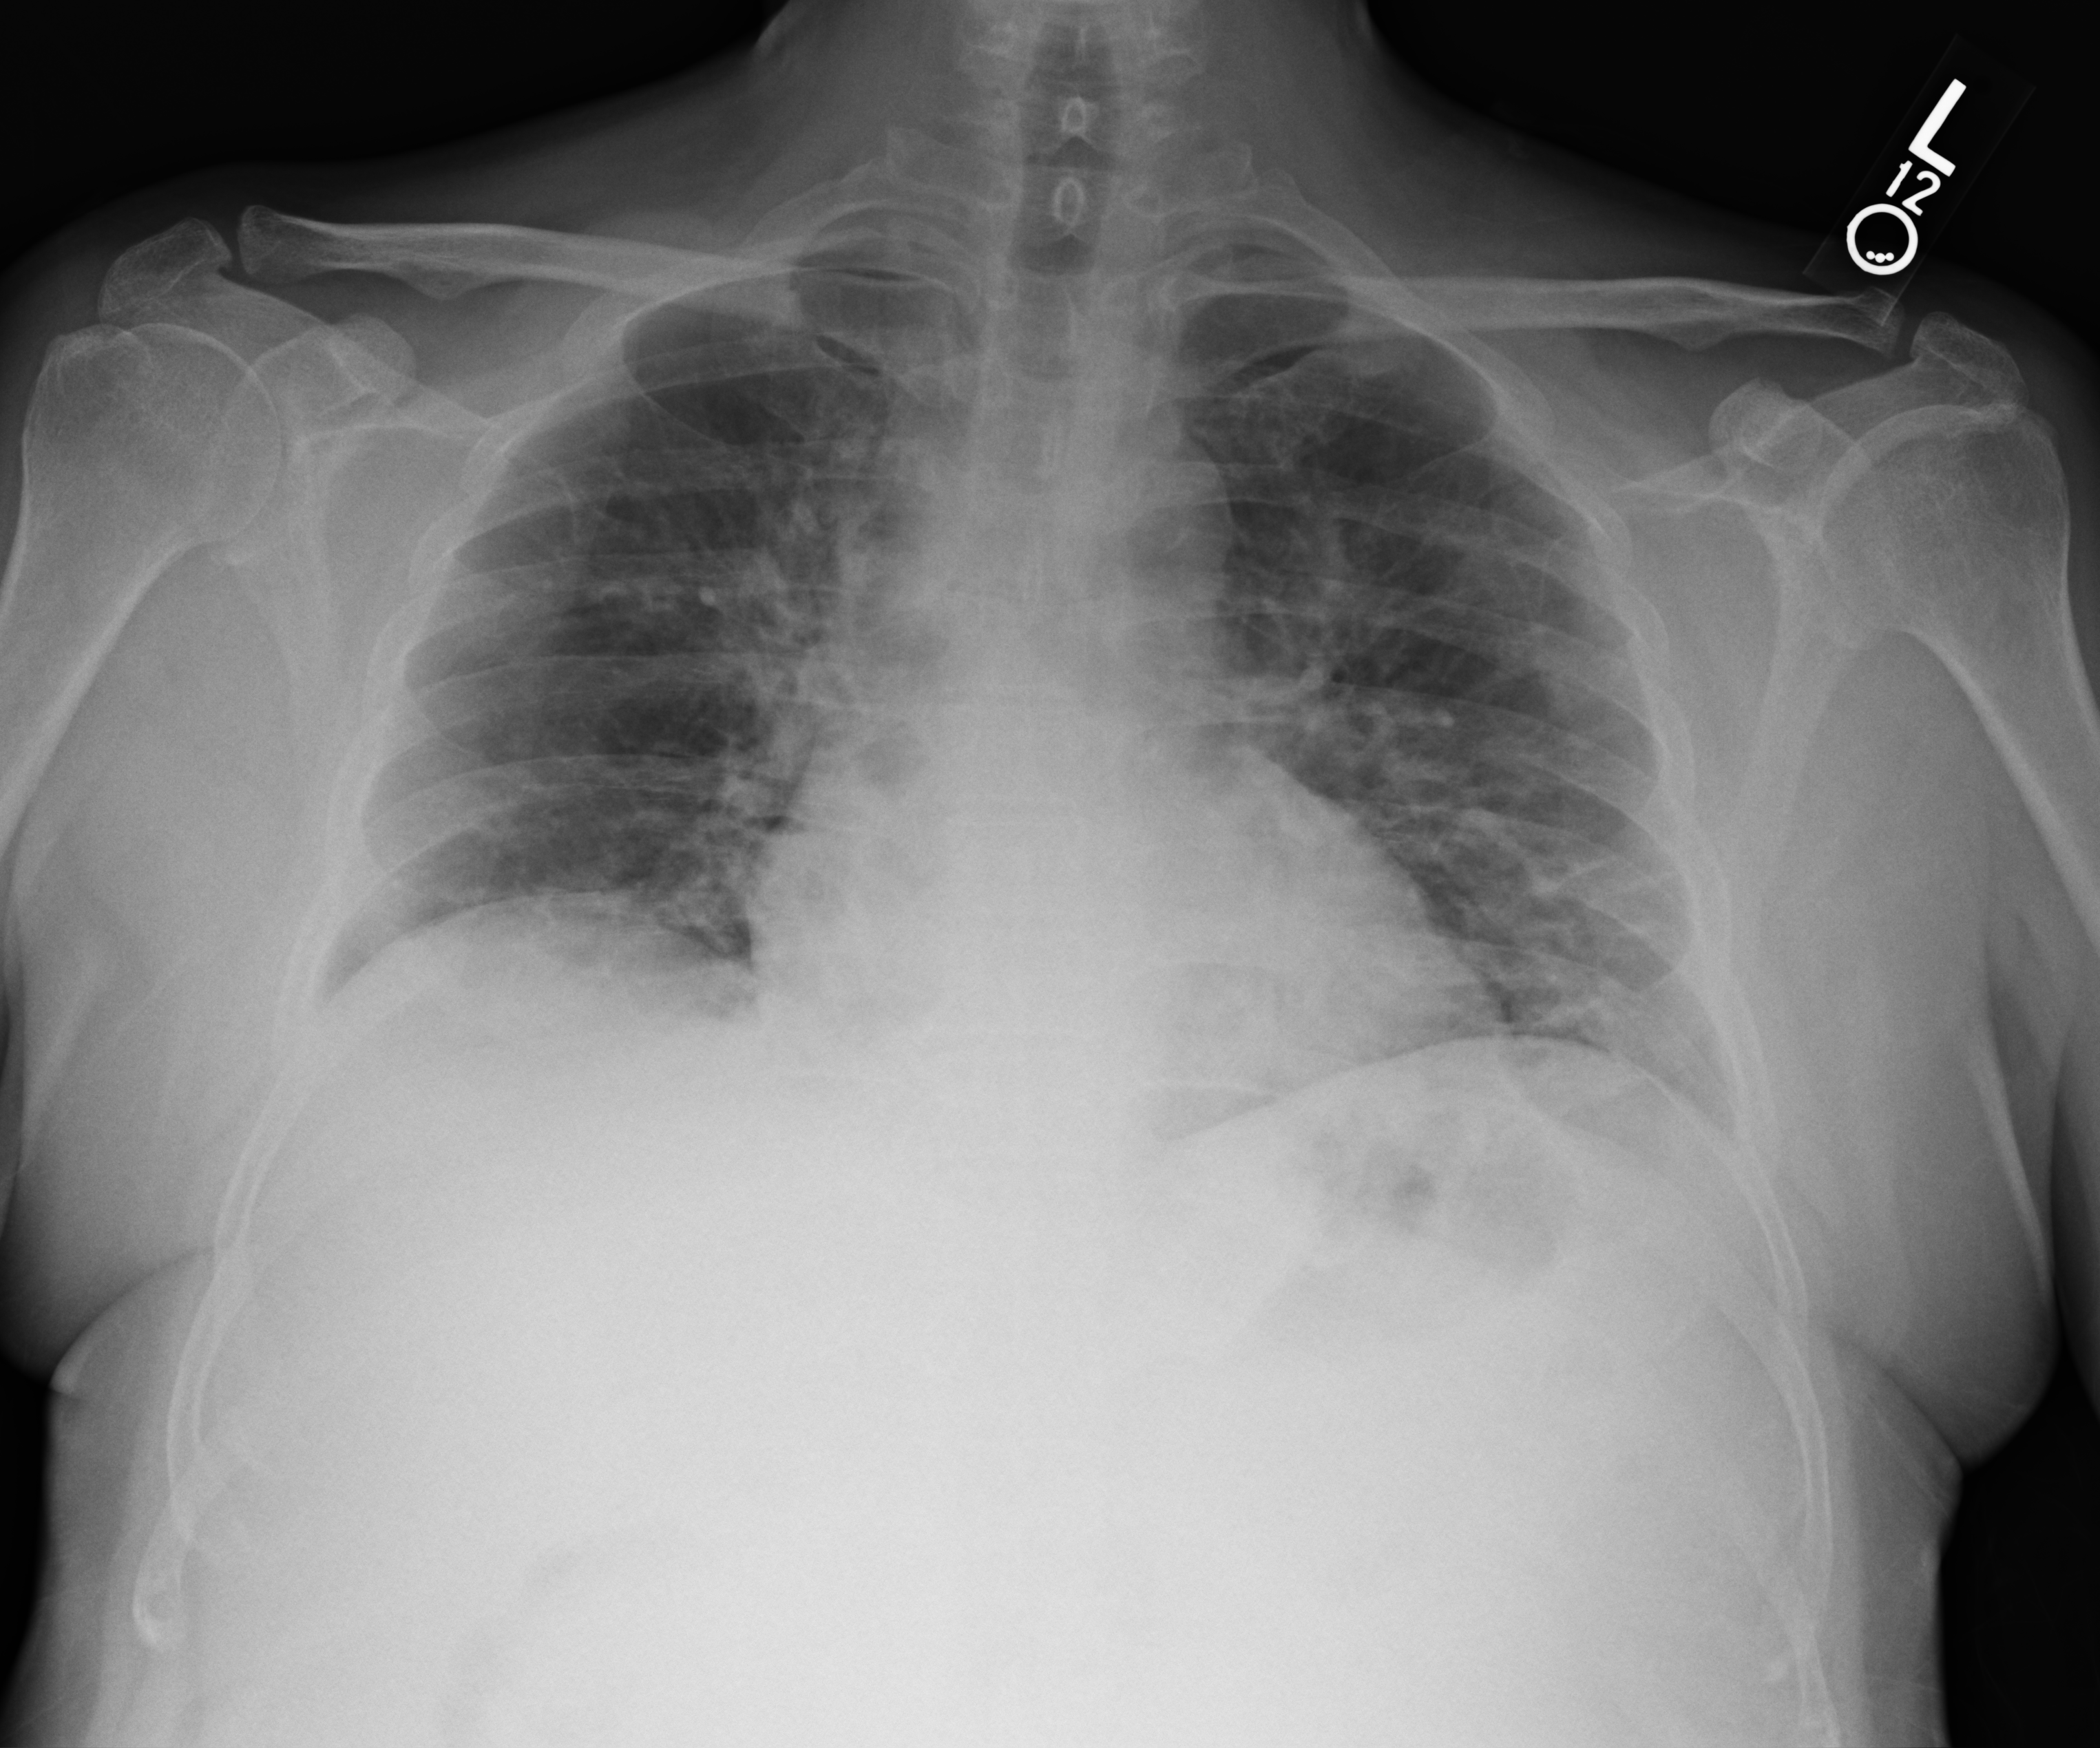
Portable chest radiograph; anteroposterior (AP) projection. Male patient hospitalised with COVID-19, age 18–59 years.
Hospital-stay facts (about this admission, not read from this image; timing relative to this image not recorded):
- admitted to intensive care during this hospital stay: no
- other chronic lung disease (admission record): no